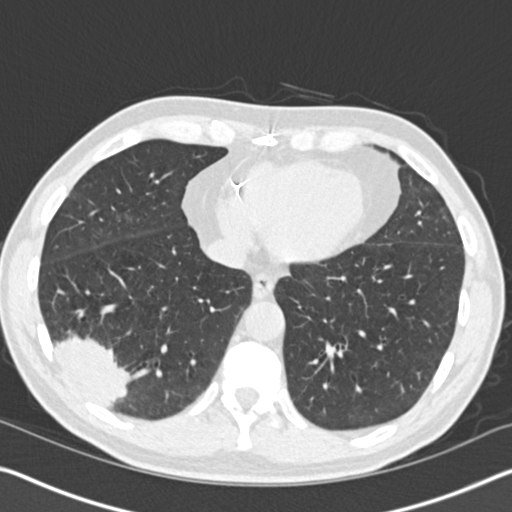
Low-dose screening chest CT, axial slice; baseline screening round; lung window (W 1500 / L -600 HU); 120 kVp; 512 × 512 image matrix. Male participant, aged 61 years at enrolment.
Expert-annotated lung lesion, bounding box (x1, y1, x2, y2) in pixels: (27, 298, 146, 418). Screening reader's record for this exam (one nodule recorded; not confirmed to be the boxed lesion): non-calcified nodule or mass ≥4 mm, right lower lobe, 52 × 36 mm, spiculated (stellate) margins, soft tissue attenuation. Official screen result: positive, change unspecified: nodule(s) >= 4 mm or enlarging nodule(s), mass(es), or other non-specific abnormalities suspicious for lung cancer.